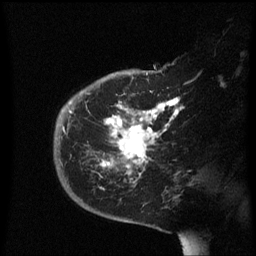
Breast MRI (dynamic contrast-enhanced), one sagittal slice. Dynamic contrast-enhanced series, image 2 of 3 at this slice position (ordered by acquisition). 1.5 T. TE 4.2 ms, TR 8.4 ms. 2.3 mm slice thickness. 256 × 256 image matrix, field of view 200 × 200 mm. Female patient, age 38 years. From the clinical record (not read from this slice): setting: breast cancer imaged before/during neoadjuvant chemotherapy; receptor status: HER2-positive.
Annotated regions visible in this slice (semi-automatically segmented with operator editing):
- analysis volume of interest (the breast-tissue region the enhancement analysis was run in; not a lesion): bounding box [x1, y1, x2, y2] px = [54, 78, 191, 213]
- tumour enhancement mask (voxels above the 70 % enhancement threshold inside the analysis volume of interest): [69, 98, 180, 189]